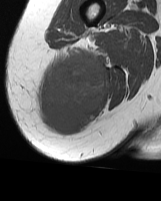
MRI of an extremity soft-tissue mass, one axial slice. Position 19 of 70 along the scan axis. MR volume resampled by the dataset authors to the PET/CT grid (not the native acquisition matrix). 3.27 mm slice thickness. 161 × 201 image matrix. Female patient. Case-level facts recorded for this patient, not image findings: histological type: synovial sarcoma; grade: intermediate; site of the primary tumour: right buttock.
Outlined on this slice (expert contour drawn on MRI and transferred to this co-registered scan by the dataset authors):
- gross tumour volume including surrounding oedema: bounding box <37,47,107,135> (left, top, right, bottom; pixels)
- gross tumour volume (mass): <38,52,107,135>